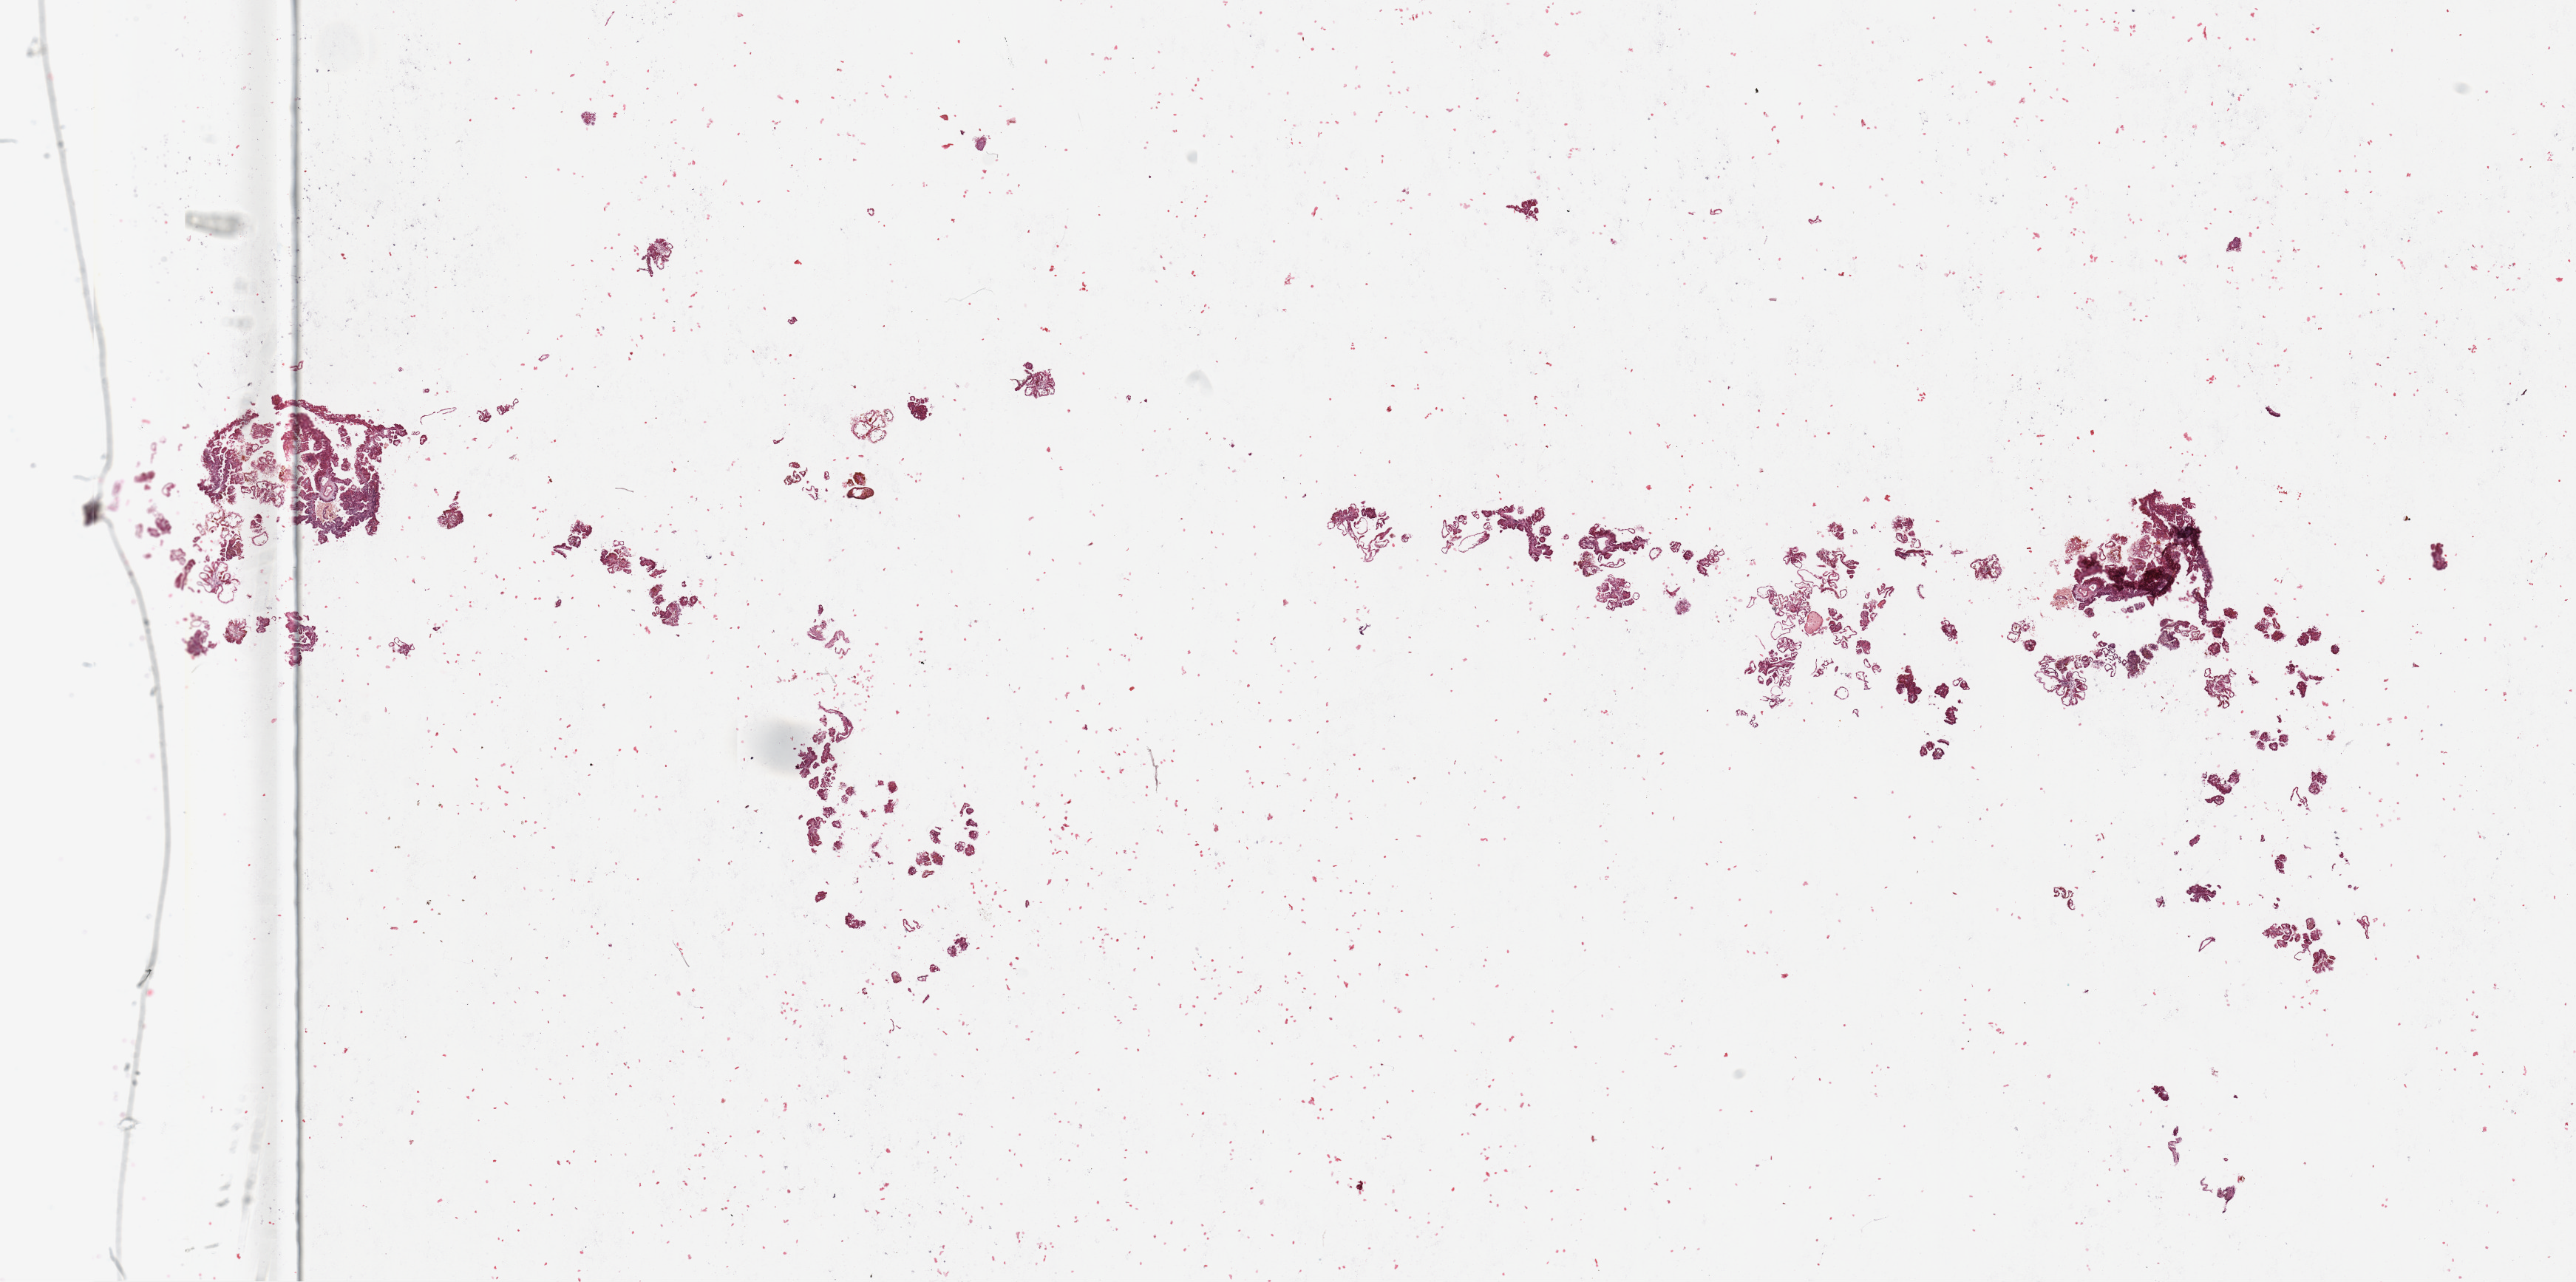
H&E whole-slide image — whole scanned area (about 27.6 x 13.7 mm, acquisition: 20x scan) shown as a low-resolution overview, tumour tissue sample, sampled site: kidney. 50-year-old male patient.
Histologic diagnosis: Renal cell carcinoma, NOS.